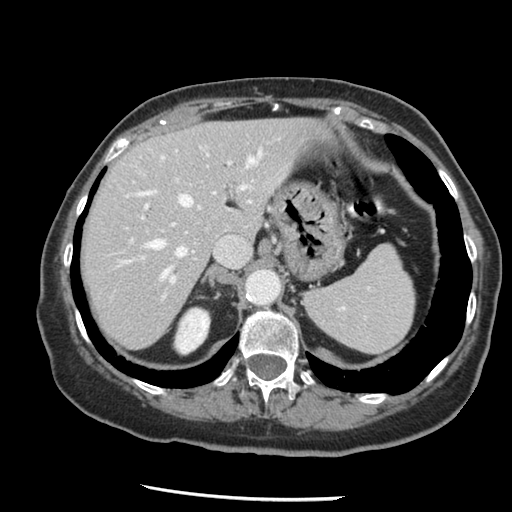
Contrast-enhanced abdominal CT, one axial slice. Slice 99 of 148 in the series (ordered by position). Reconstruction kernel STANDARD. 120 kVp. Intravenous contrast given. Soft-tissue window (W 400 / L 40 HU). 2.5 mm slice thickness. 512 × 512 image matrix, field of view 330 × 330 mm. Female patient, age 85 years. Case-level facts recorded for this patient, not image findings: diagnosis: colorectal cancer liver metastases, imaged before liver resection.
Outlined on this slice (expert manual segmentation):
- hepatic veins: bounding box <124,146,264,279> (left, top, right, bottom; pixels)
- liver: <82,119,316,349>
- planned liver remnant (the part of the liver to remain after resection): <82,119,316,349>
- portal vein (with intrahepatic branches): <130,160,249,299>